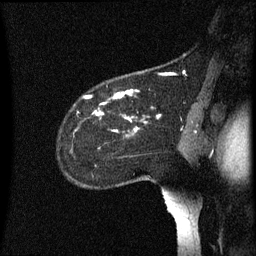
Breast MRI (dynamic contrast-enhanced), one sagittal slice; slice 47 of 60 in the series (ordered by position); dynamic contrast-enhanced series, image 2 of 3 at this slice position (ordered by acquisition); 1.5 T; TE 4.2 ms, TR 8.4 ms; 2.2 mm slice thickness; 256 × 256 image matrix. Patient: female, 35 years. Case-level facts recorded for this patient, not image findings: setting: breast cancer imaged before/during neoadjuvant chemotherapy; receptor status: HER2-positive.
Annotated regions visible in this slice (semi-automatically segmented with operator editing):
- analysis volume of interest (the breast-tissue region the enhancement analysis was run in; not a lesion): bounding box <60,72,163,167> (left, top, right, bottom; pixels)
- tumour enhancement mask (voxels above the 70 % enhancement threshold inside the analysis volume of interest): <84,90,140,133>